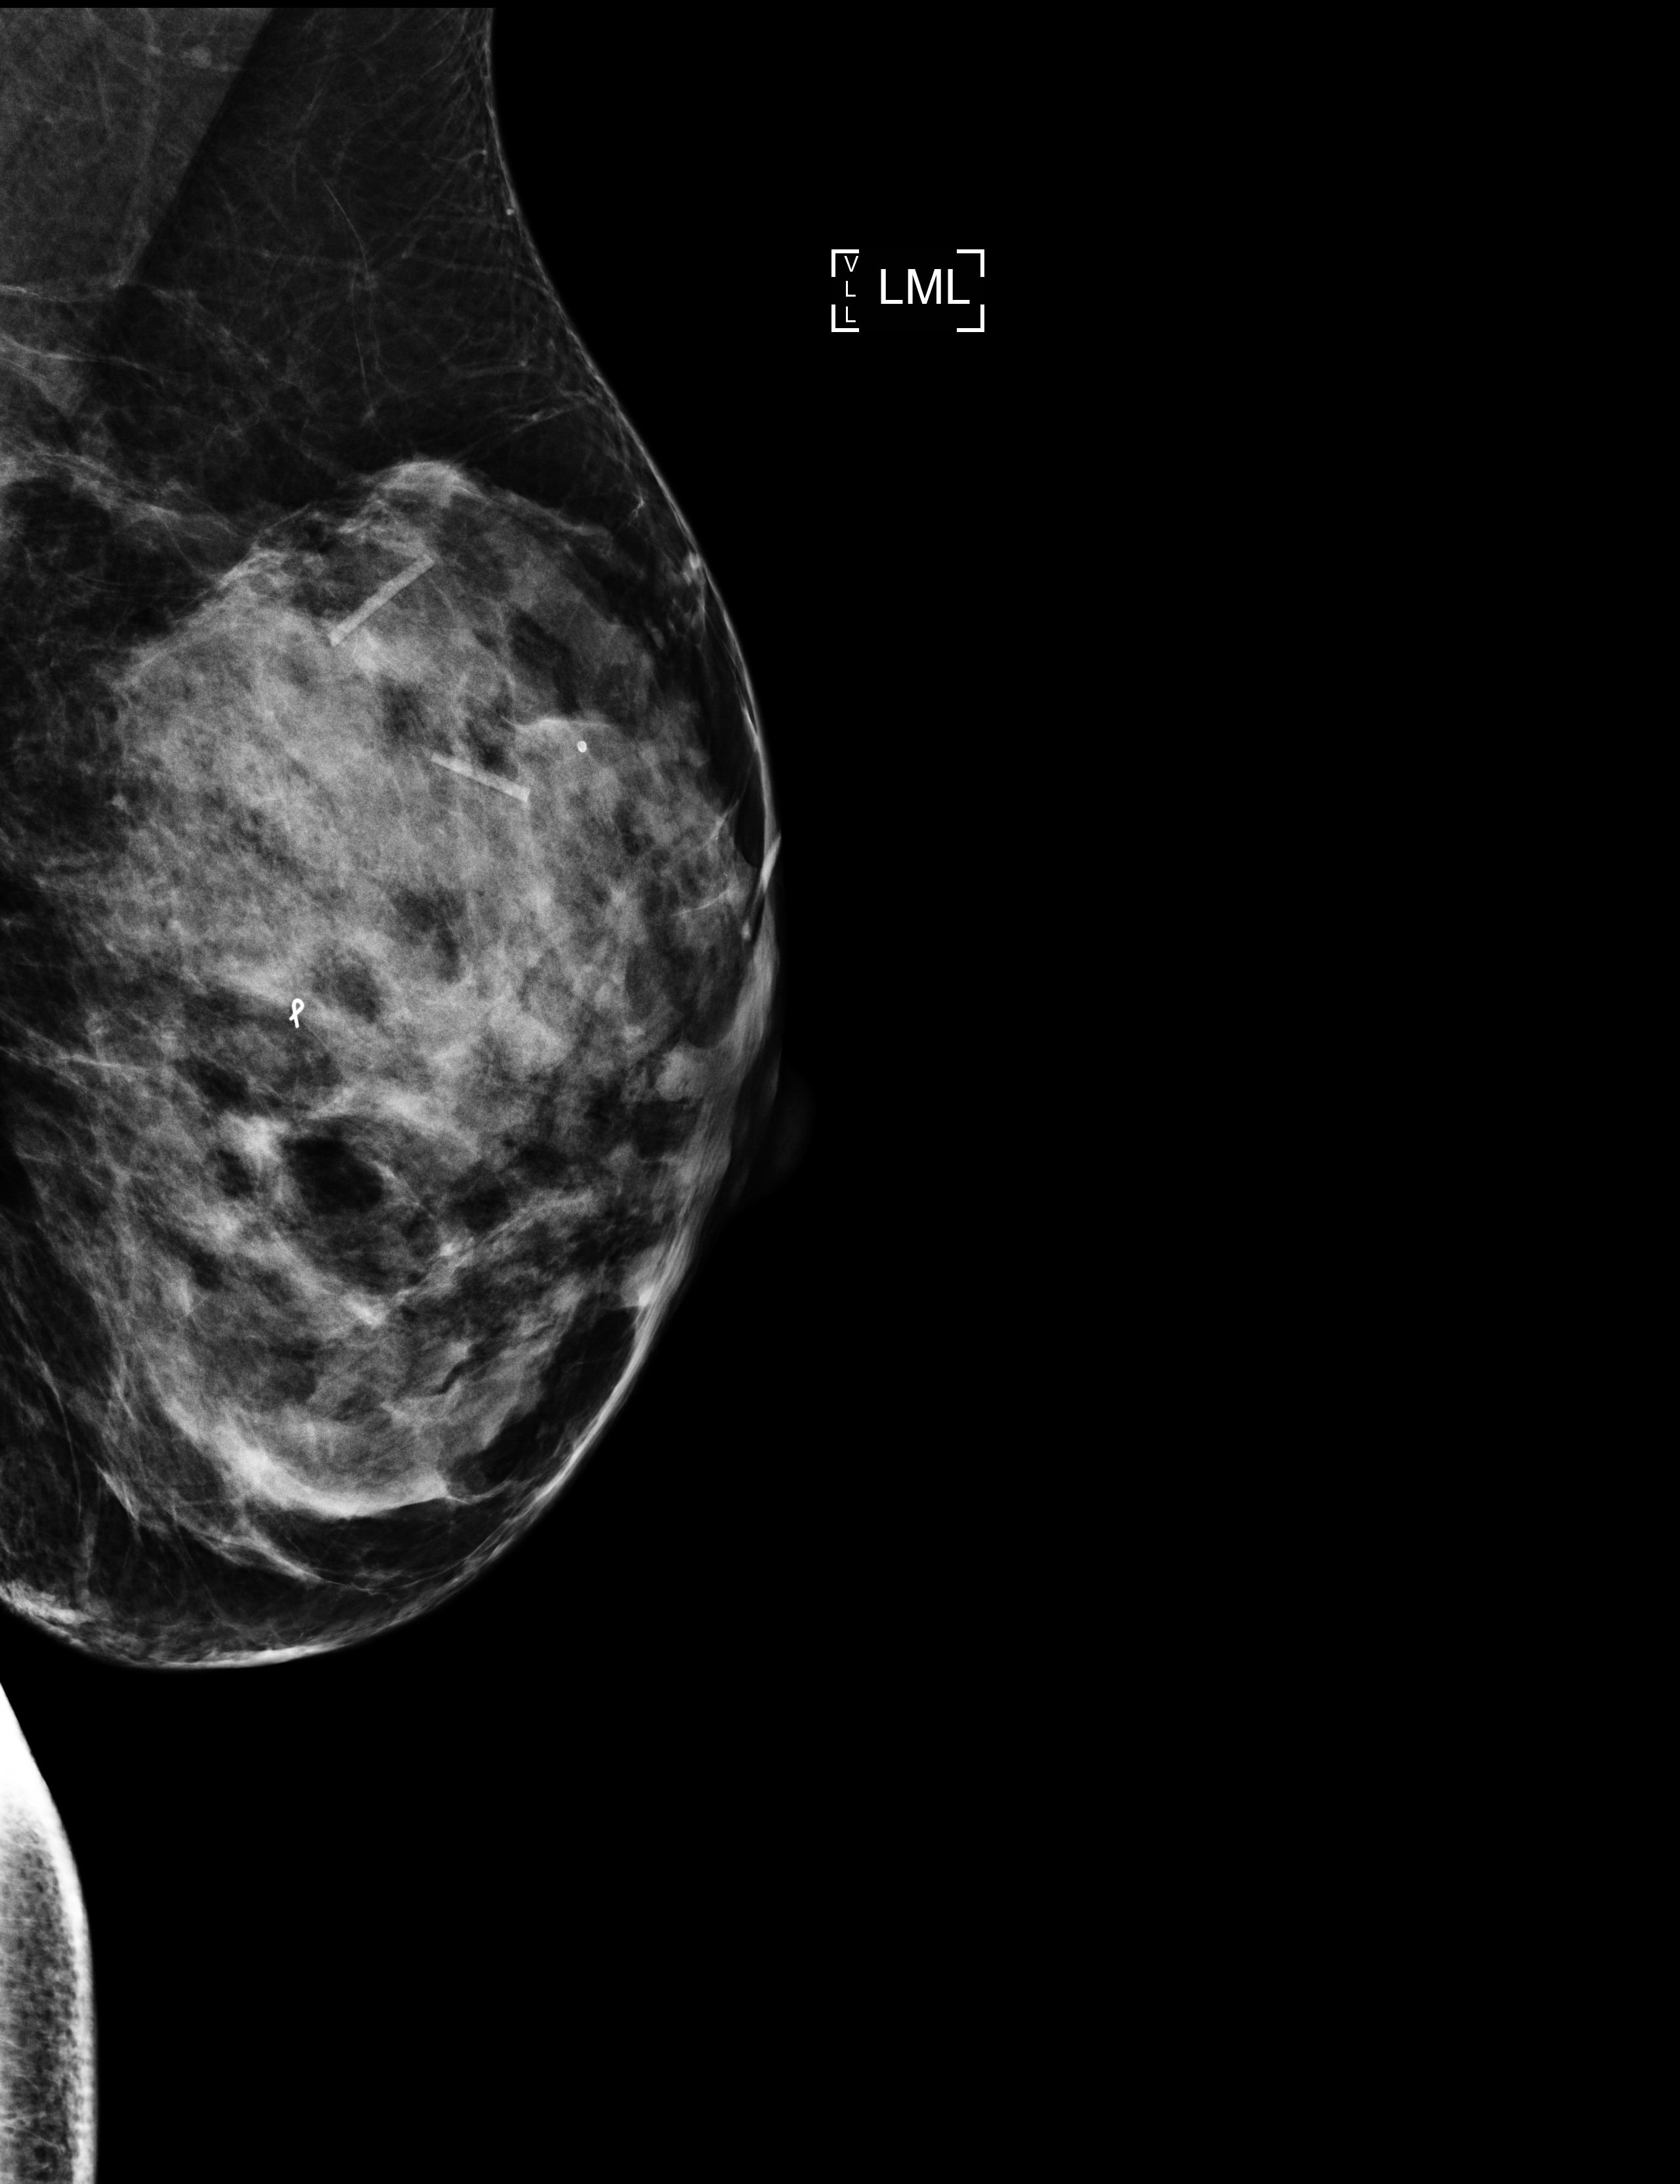
Diagnostic examination (additional views), compressed breast thickness 55 mm. Patient aged 48 years (female).
Image type: full-field digital mammogram. Breast: left. Projection: ML view.